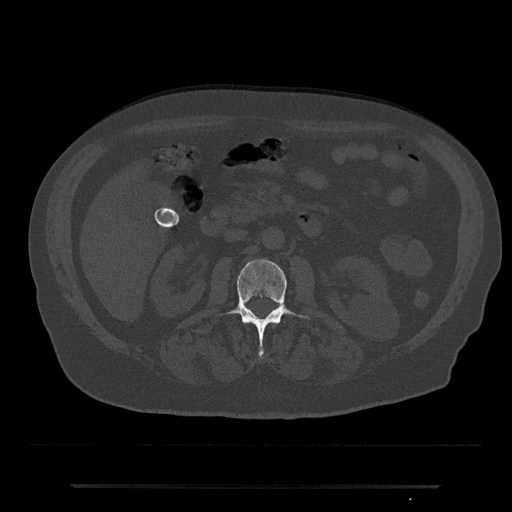
CT including the spine, one axial slice; slice 471 of 797 in the series (ordered by position); 120 kVp; bone window (W 1800 / L 400 HU); 0.5 mm slice thickness; 512 × 512 image matrix. Patient: male, 80 years. From the clinical record (not read from this slice): primary cancer: prostate.
Outlined on this slice (semi-automatic segmentation, software-assisted and operator-edited):
- L2 vertebra: box from (x=229, y=259) to (x=302, y=359) px